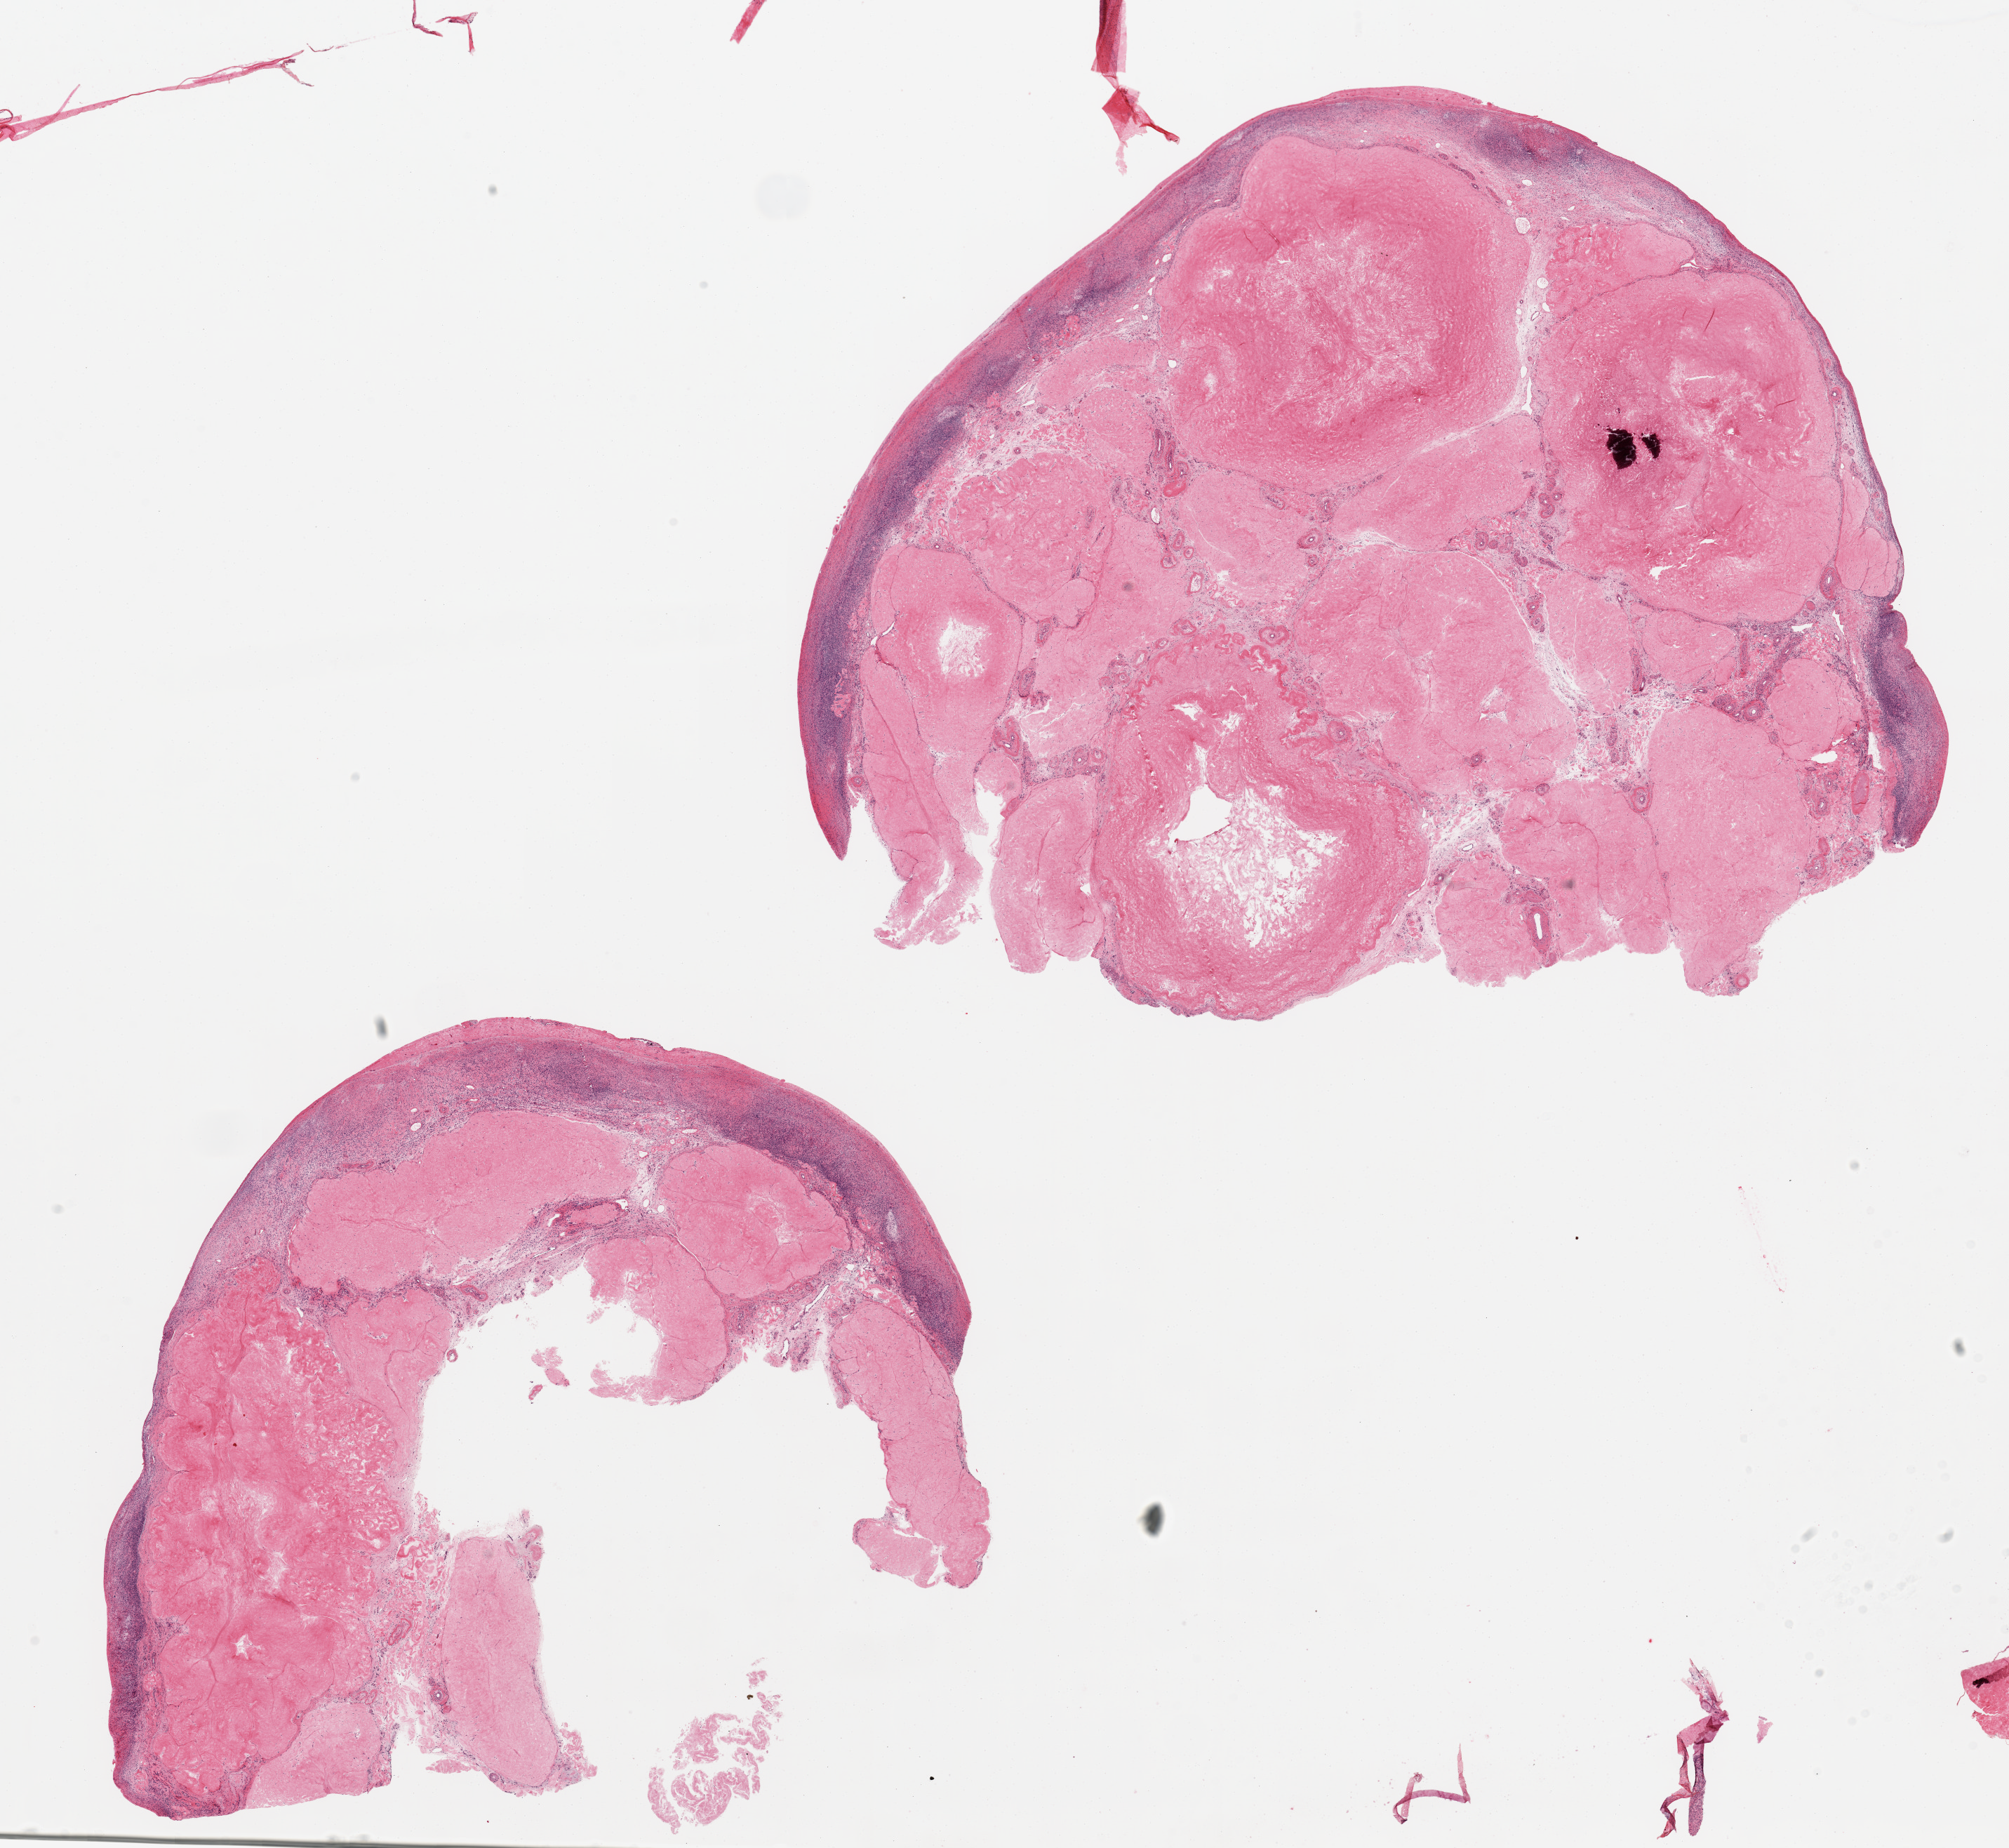
Haematoxylin and eosin whole-slide image, brightfield — shown as a low-resolution overview of the whole scanned area (about 22.6 x 20.8 mm, from a 20x scan); PAXgene-fixed, paraffin-embedded tissue; section of ovary (target tissue); tissue donor sample. Donor sex: female.
Pathologist's review note for this sample: 2 pieces, typical post menopausal atrophy with prominent corpora albicantia.